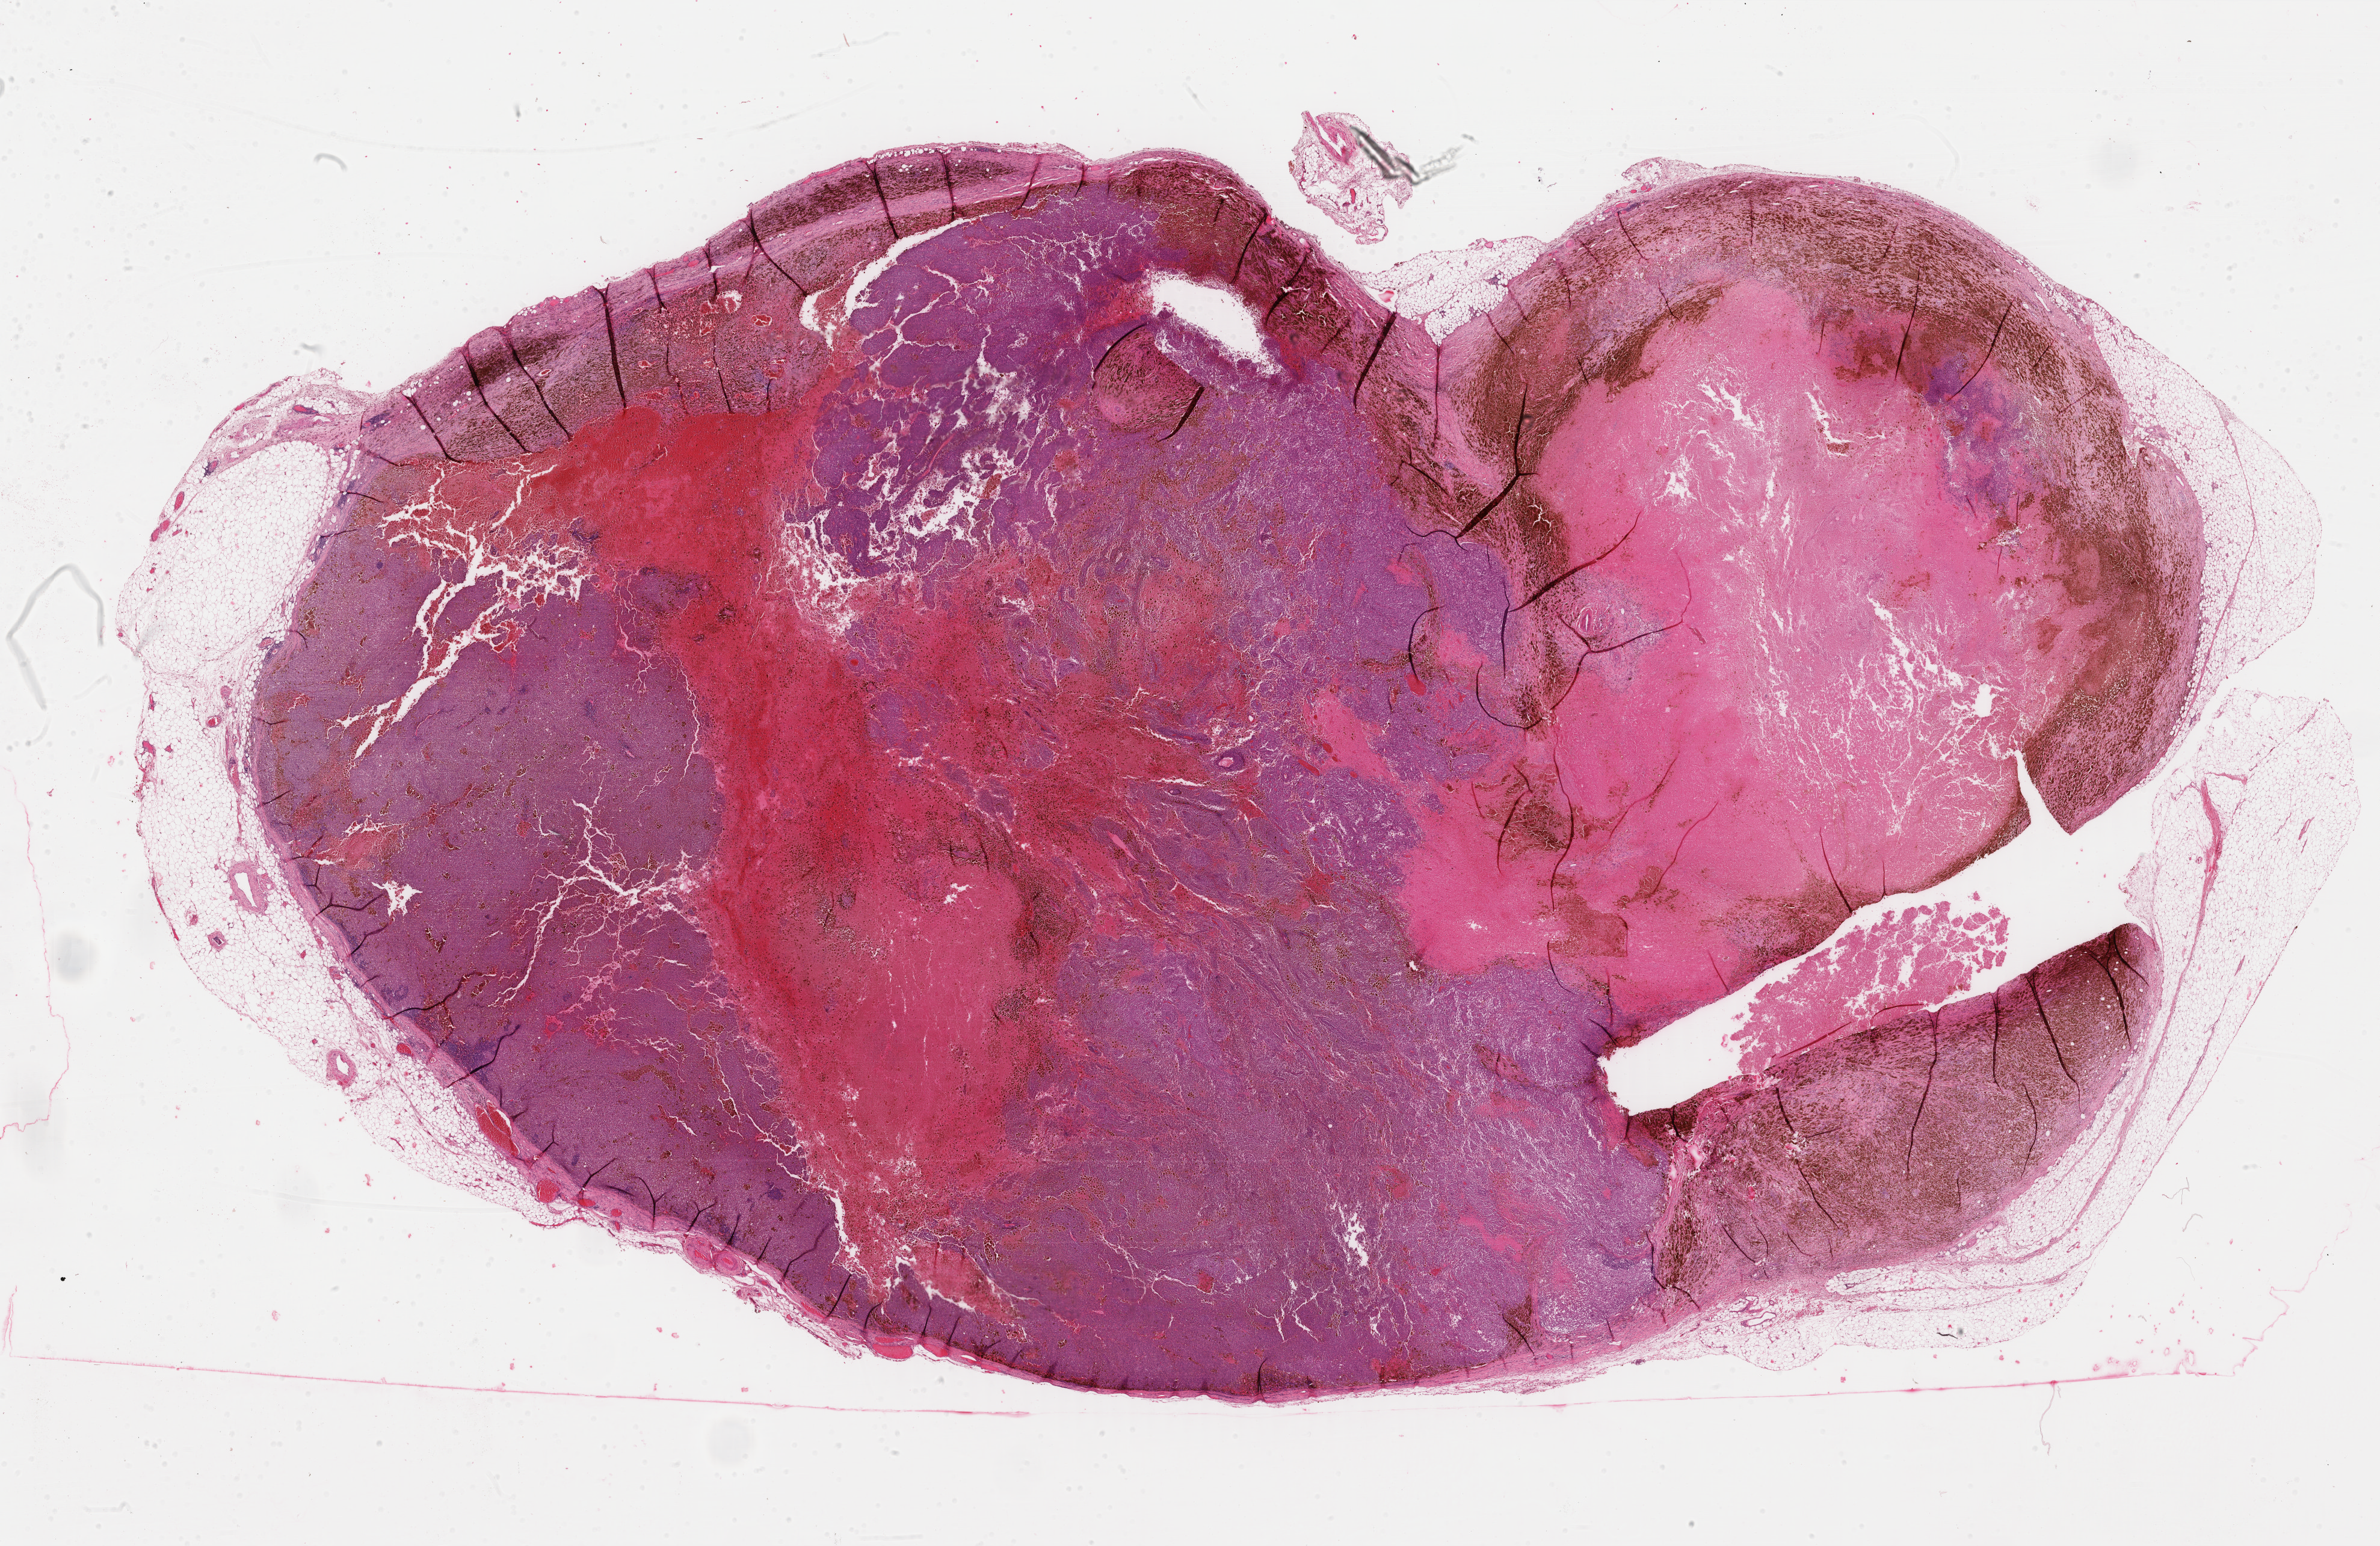
Hematoxylin and eosin (H&E) stained whole-slide image, shown as a low-resolution overview of the whole scanned area (about 31.4 x 20.4 mm). Formalin-fixed paraffin-embedded (FFPE) diagnostic section. Skin, primary tumour sample. Male, age 54 years at initial diagnosis.
Diagnosis: Malignant melanoma, NOS.